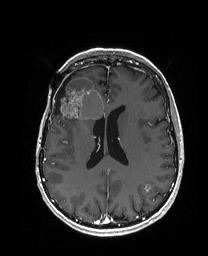
Brain MRI from a brain-tumour surgery series, one axial slice; position 78 of 192 along the scan axis; T1-weighted post-contrast; 1 mm slice thickness; 208 × 256 image matrix, field of view 203 × 250 mm. Case-level facts recorded for this patient, not image findings: histopathology: Metastatic Carcinoma from Breast primary.
Structures marked on this image (manually delineated by an expert):
- previous resection cavity: bounding box (x1, y1, x2, y2) in pixels: (54, 77, 71, 115)
- tumour: (55, 77, 104, 128)